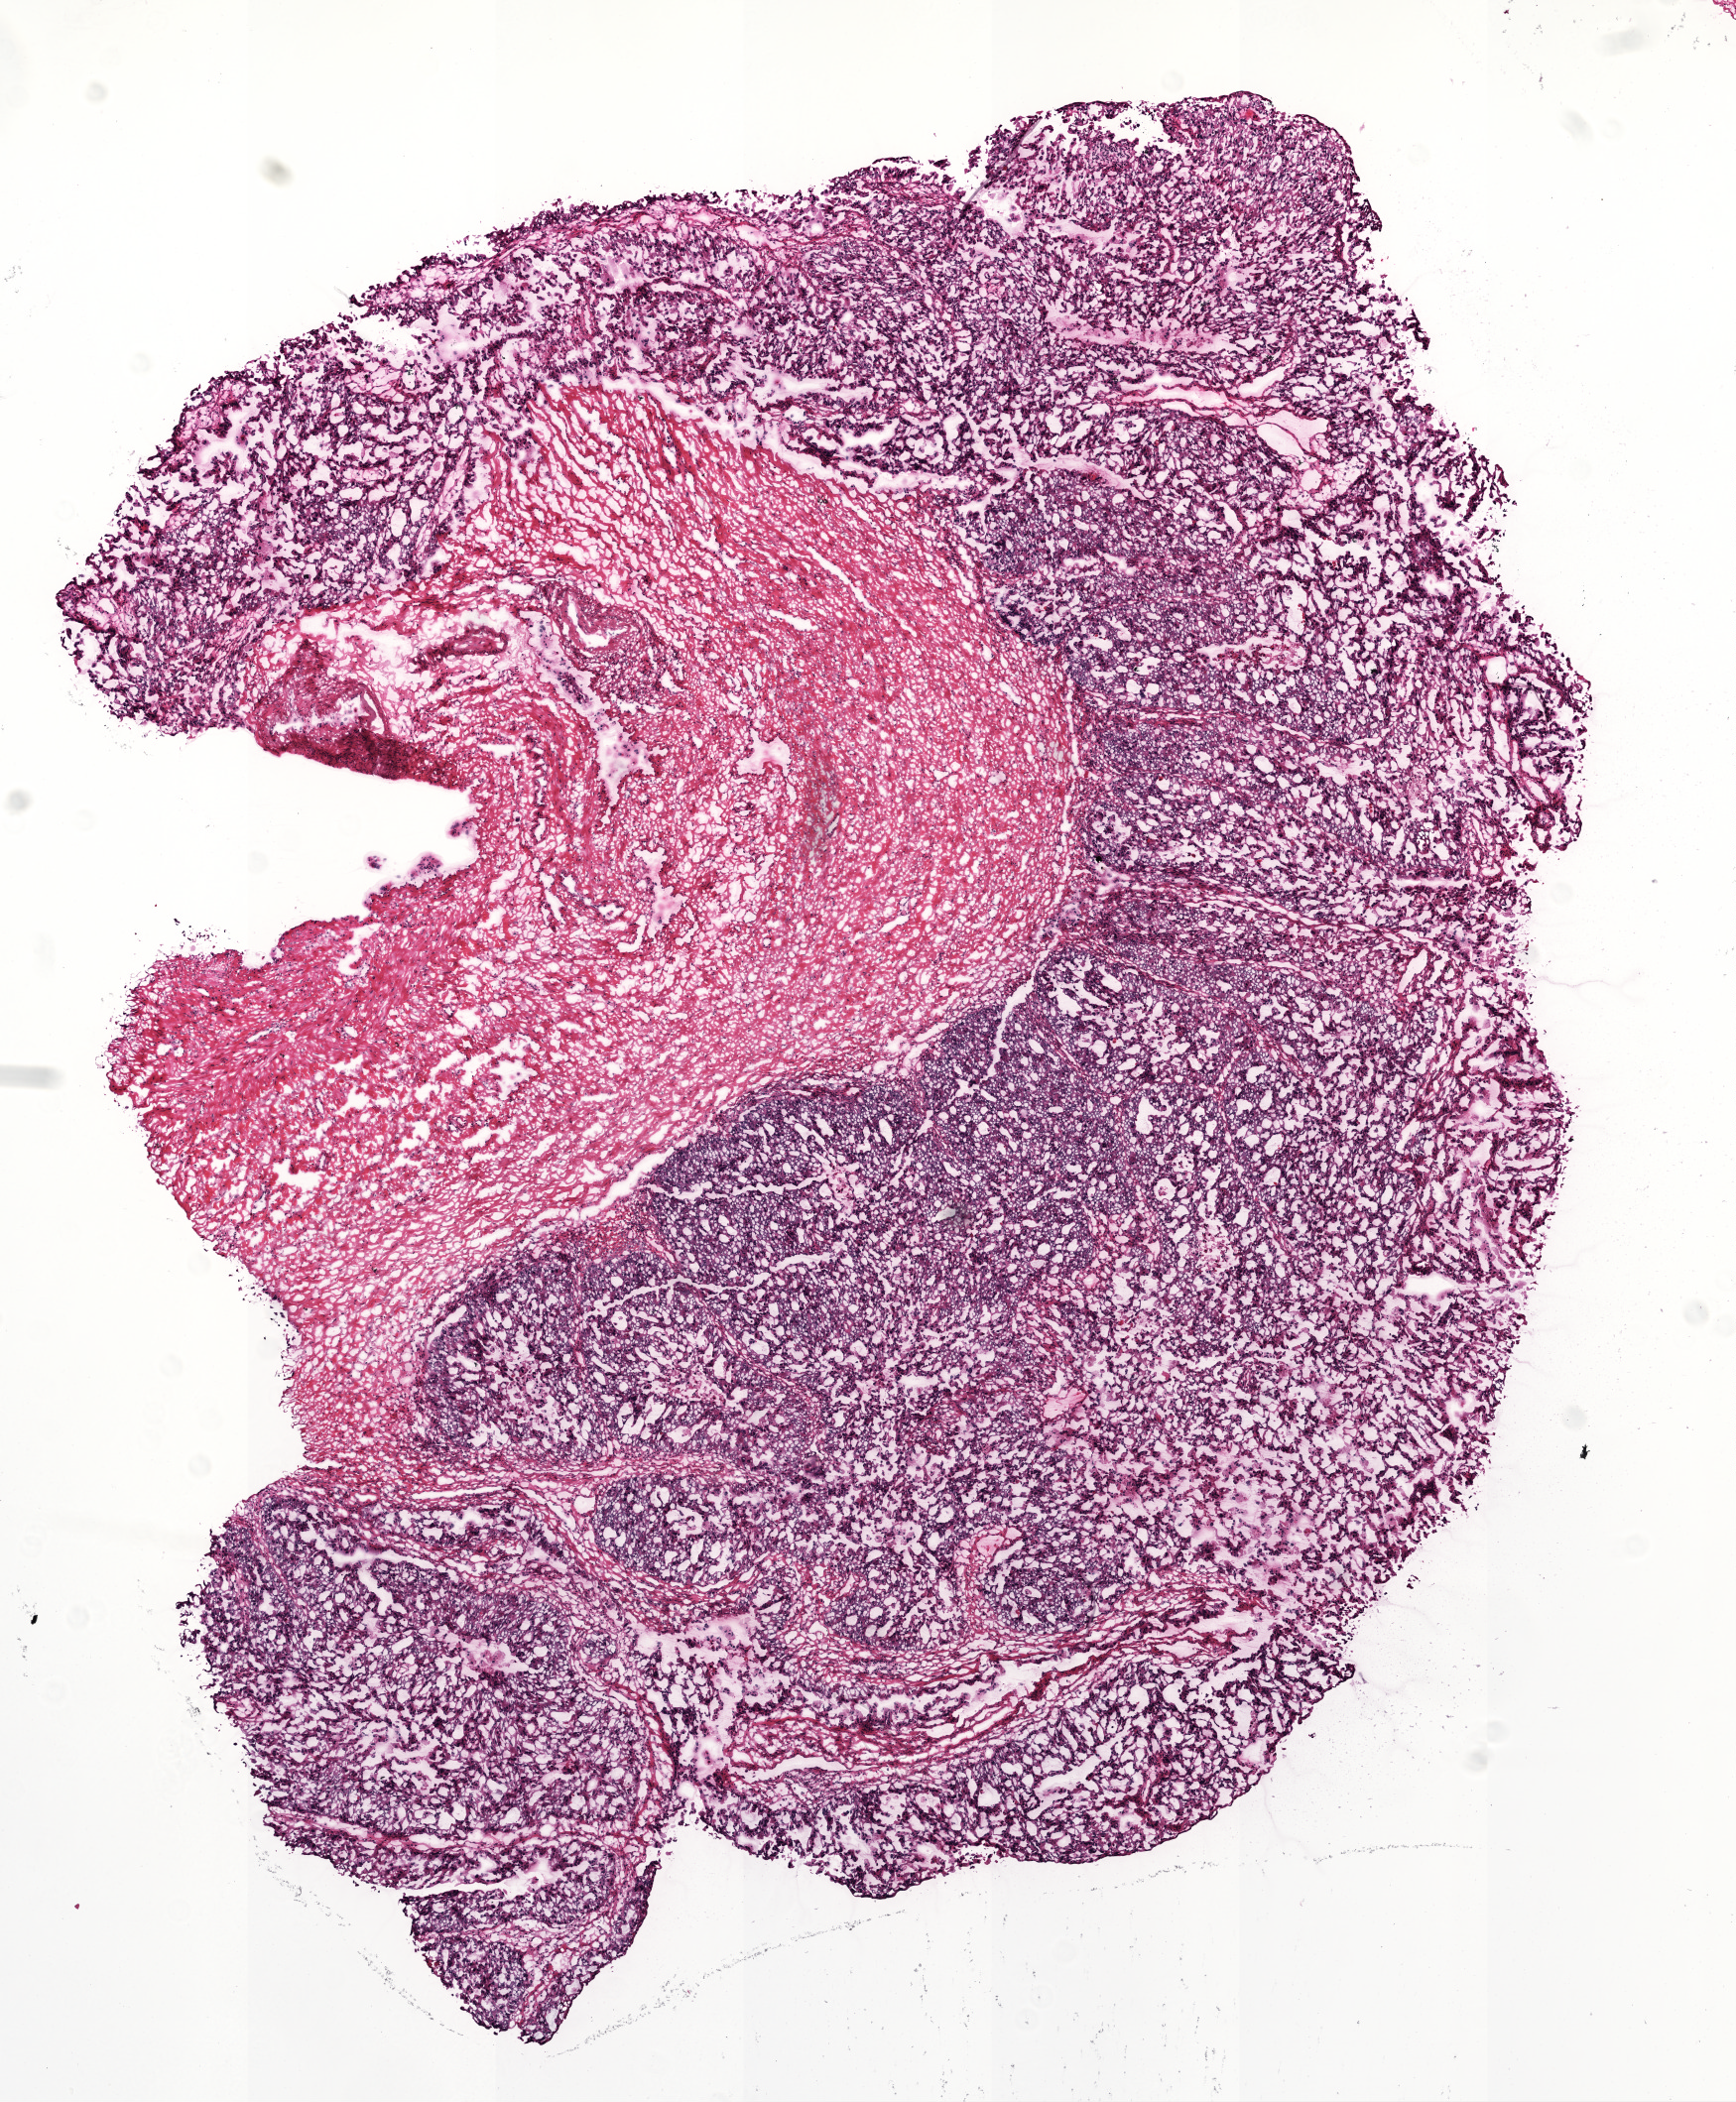
Whole-slide histology image, H&E, whole scanned area (about 7.0 x 8.5 mm) shown as a low-resolution overview; frozen section from the top of the tissue portion; ovary, primary tumour sample. Female patient; age at initial diagnosis 75 years.
Pathologic diagnosis: Serous cystadenocarcinoma, NOS.